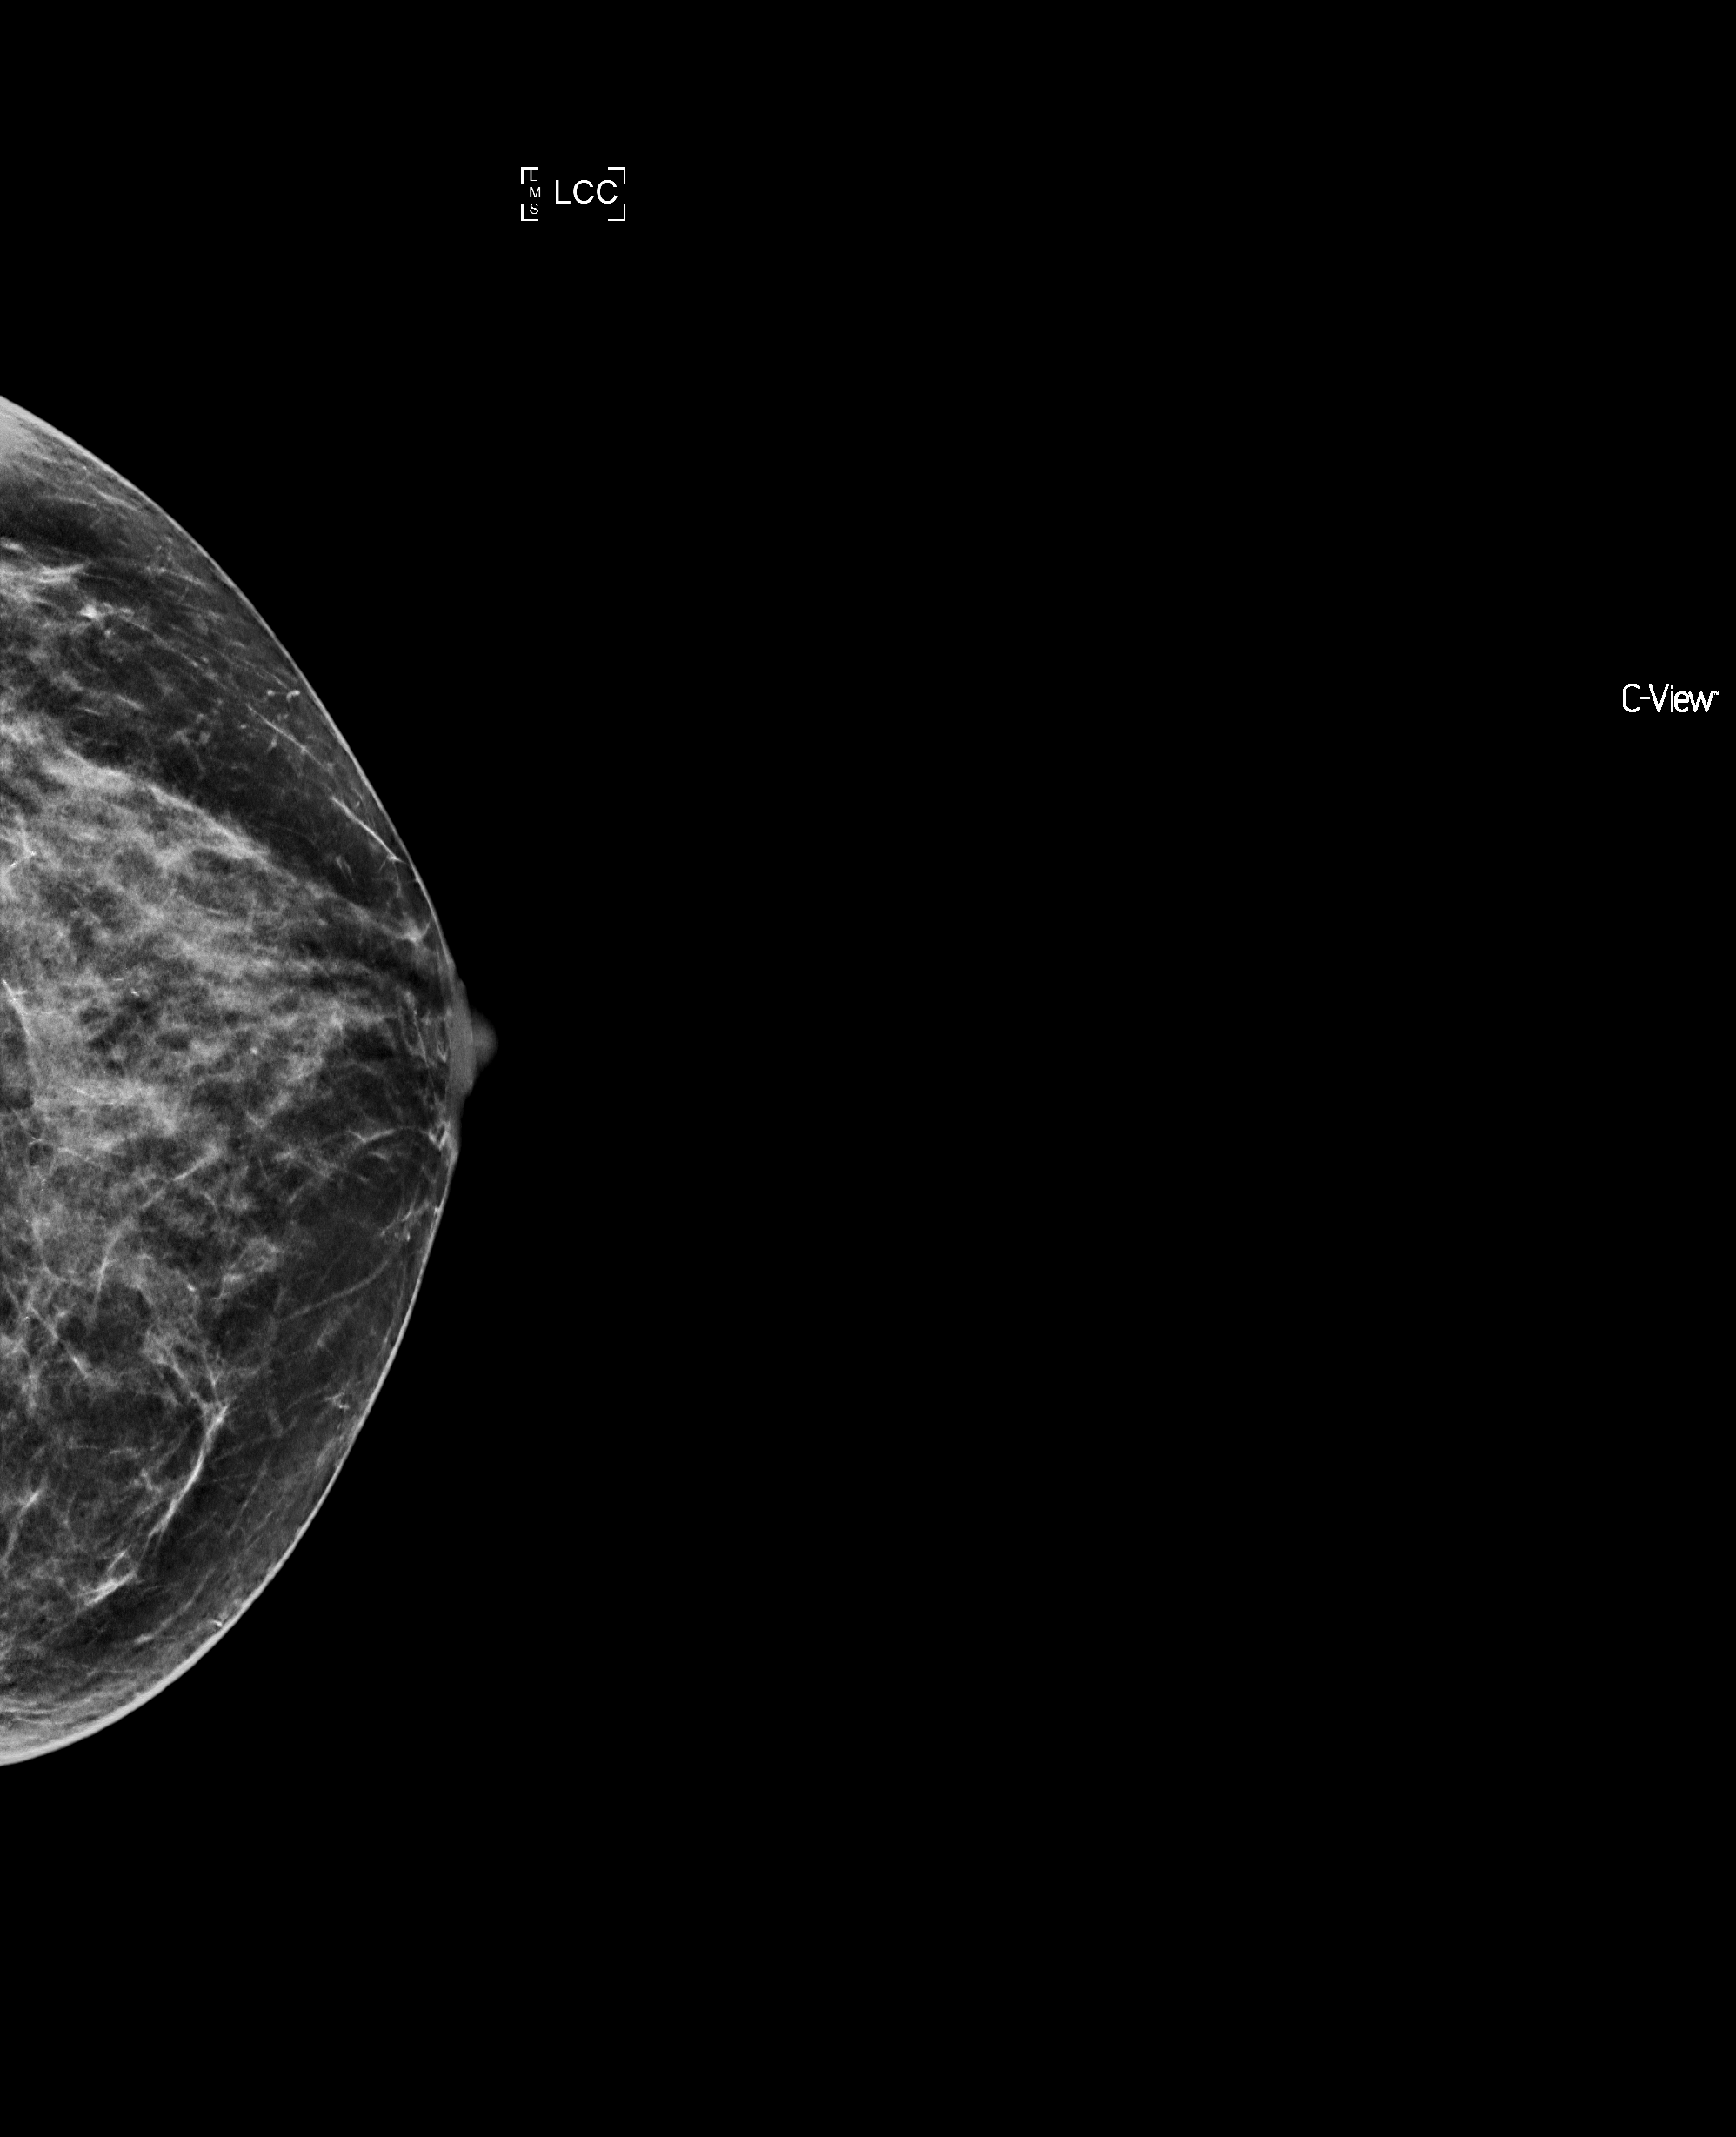
Digital mammogram (FFDM); left breast; cranio-caudal projection; annual screening mammography examination; compressed breast thickness 49 mm. Female patient, age 59 years.
BI-RADS breast density category at the screening exam (both breasts, scale 1–4): 3. Final BI-RADS assessment for this screening round (tomosynthesis exam, both breasts): category 1. Recall: no recall after this screen.